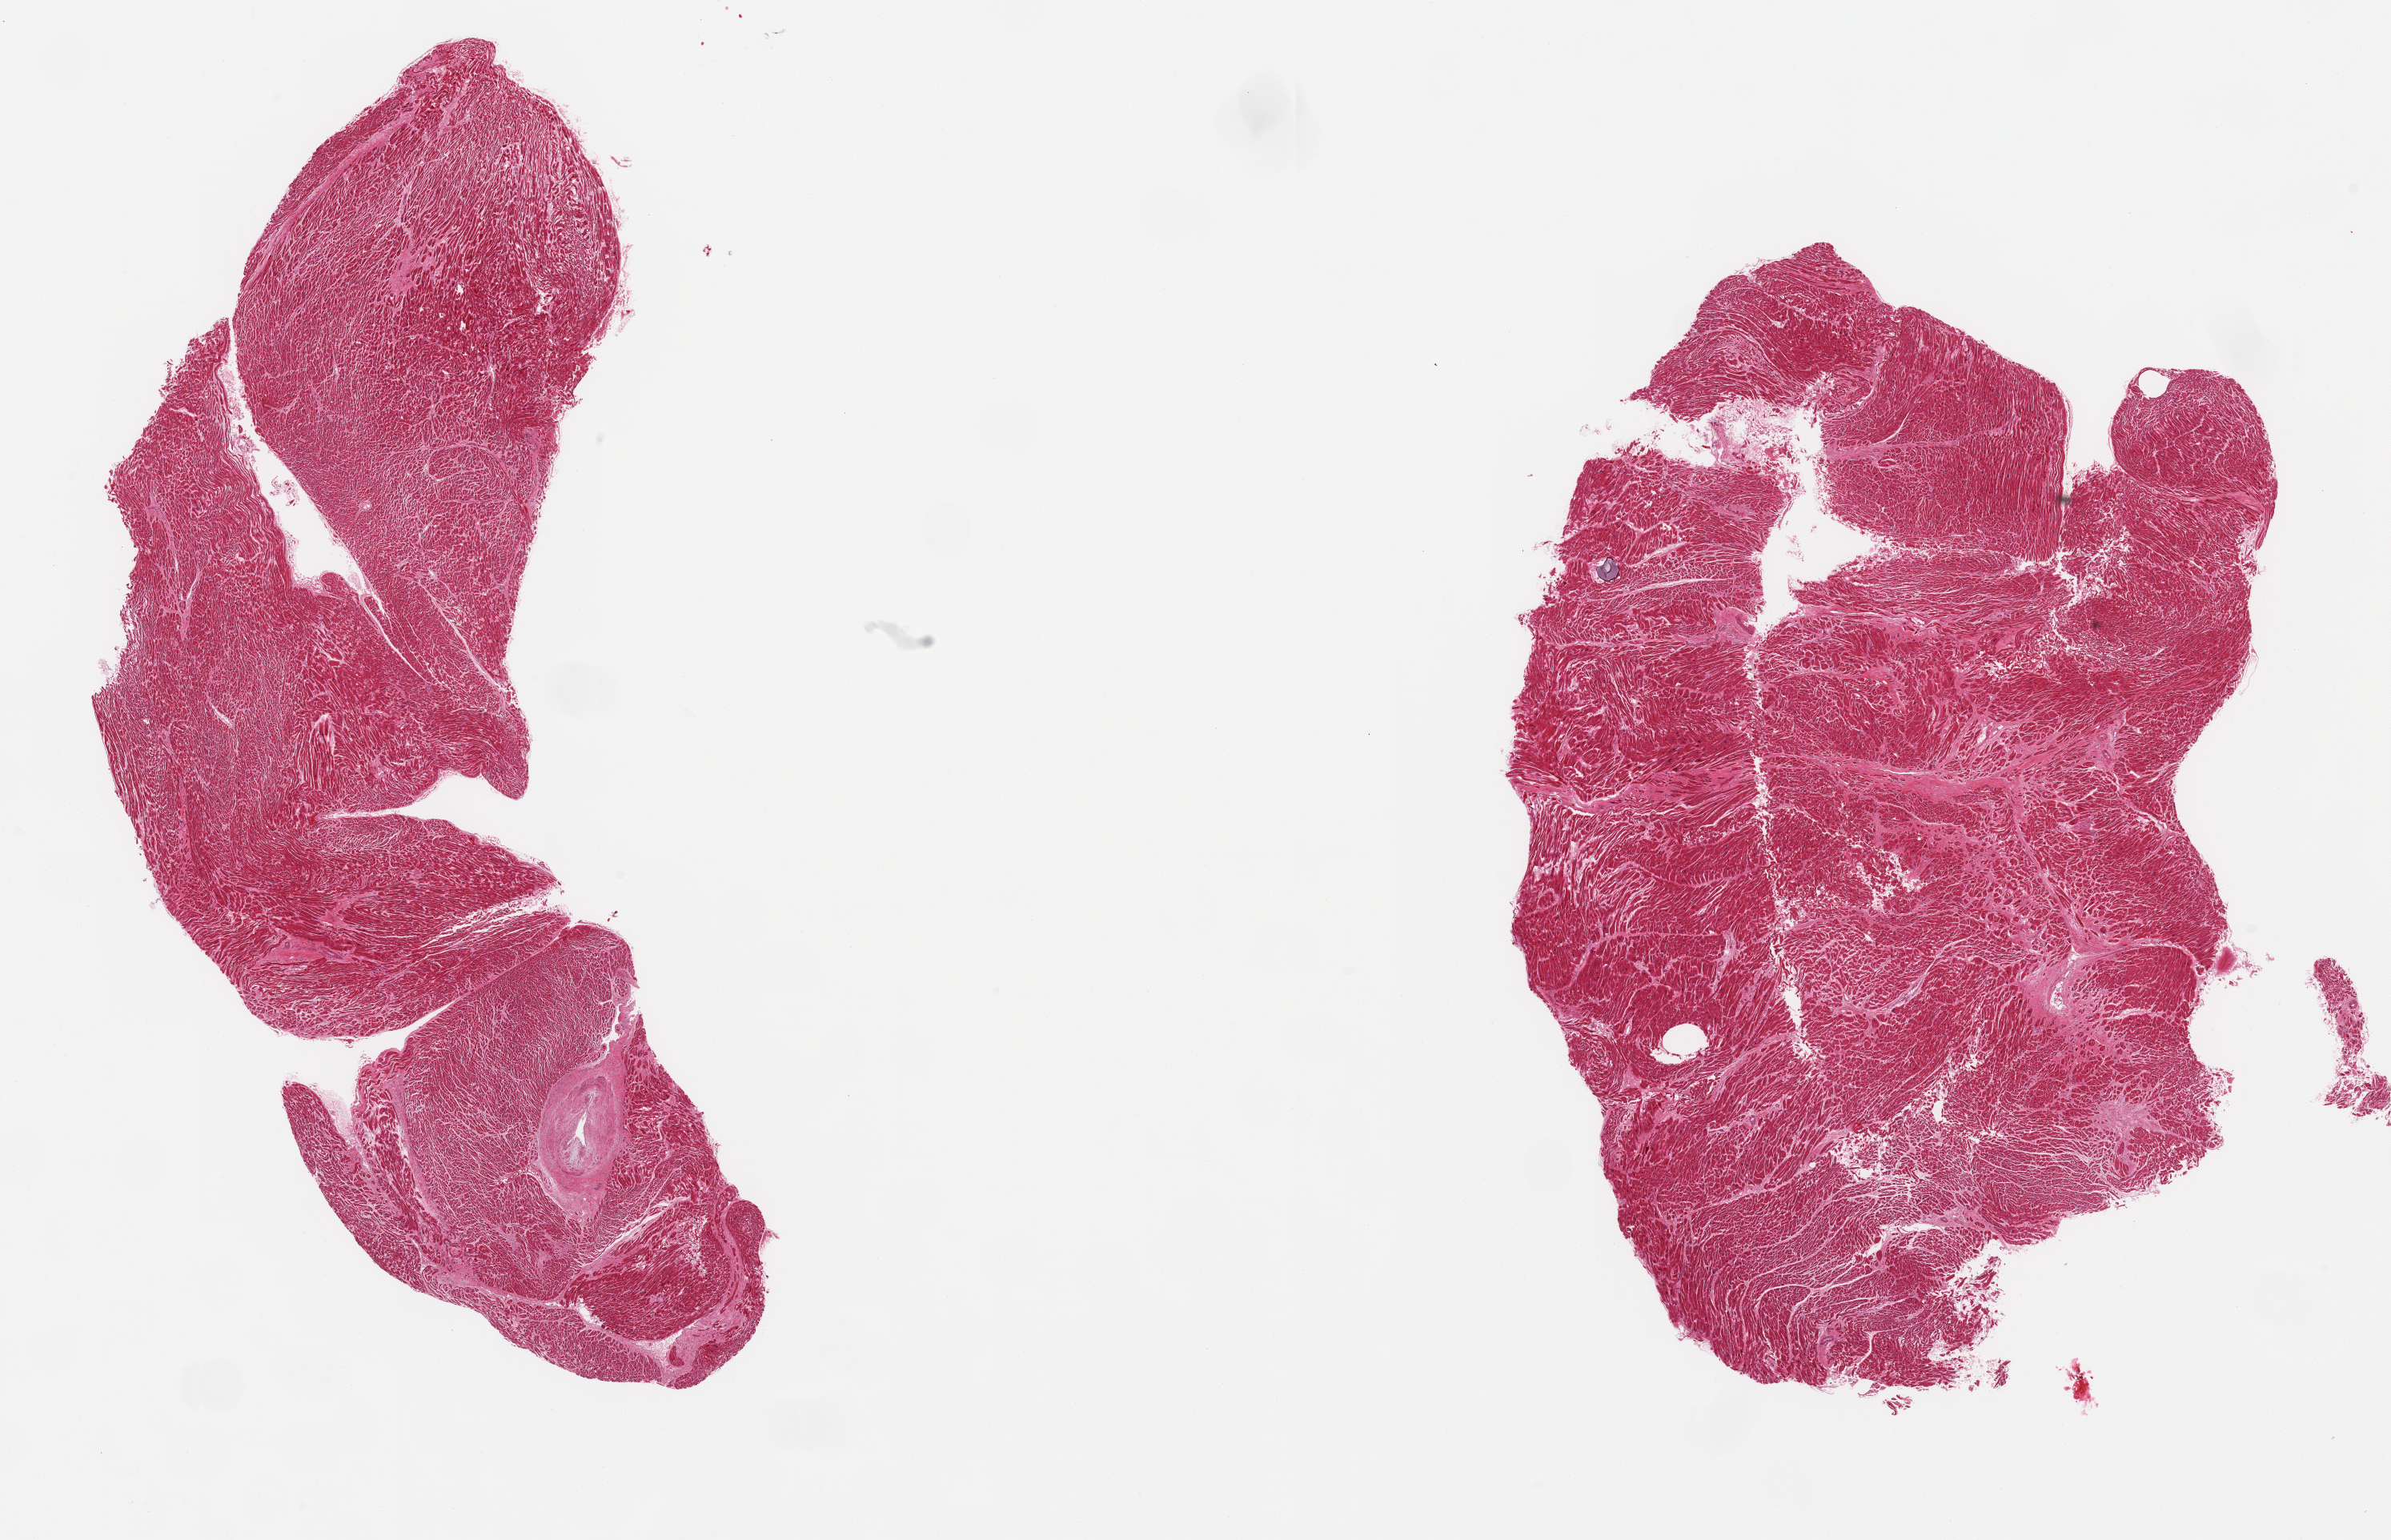
Whole-slide image, hematoxylin and eosin (H&E) stain, brightfield, shown as a low-resolution overview of the whole scanned area (about 23.6 x 15.2 mm, acquisition: 20x scan).
Specimen: PAXgene-fixed paraffin-embedded (PFPE) section; sampled site (target tissue): heart; donor tissue sample.